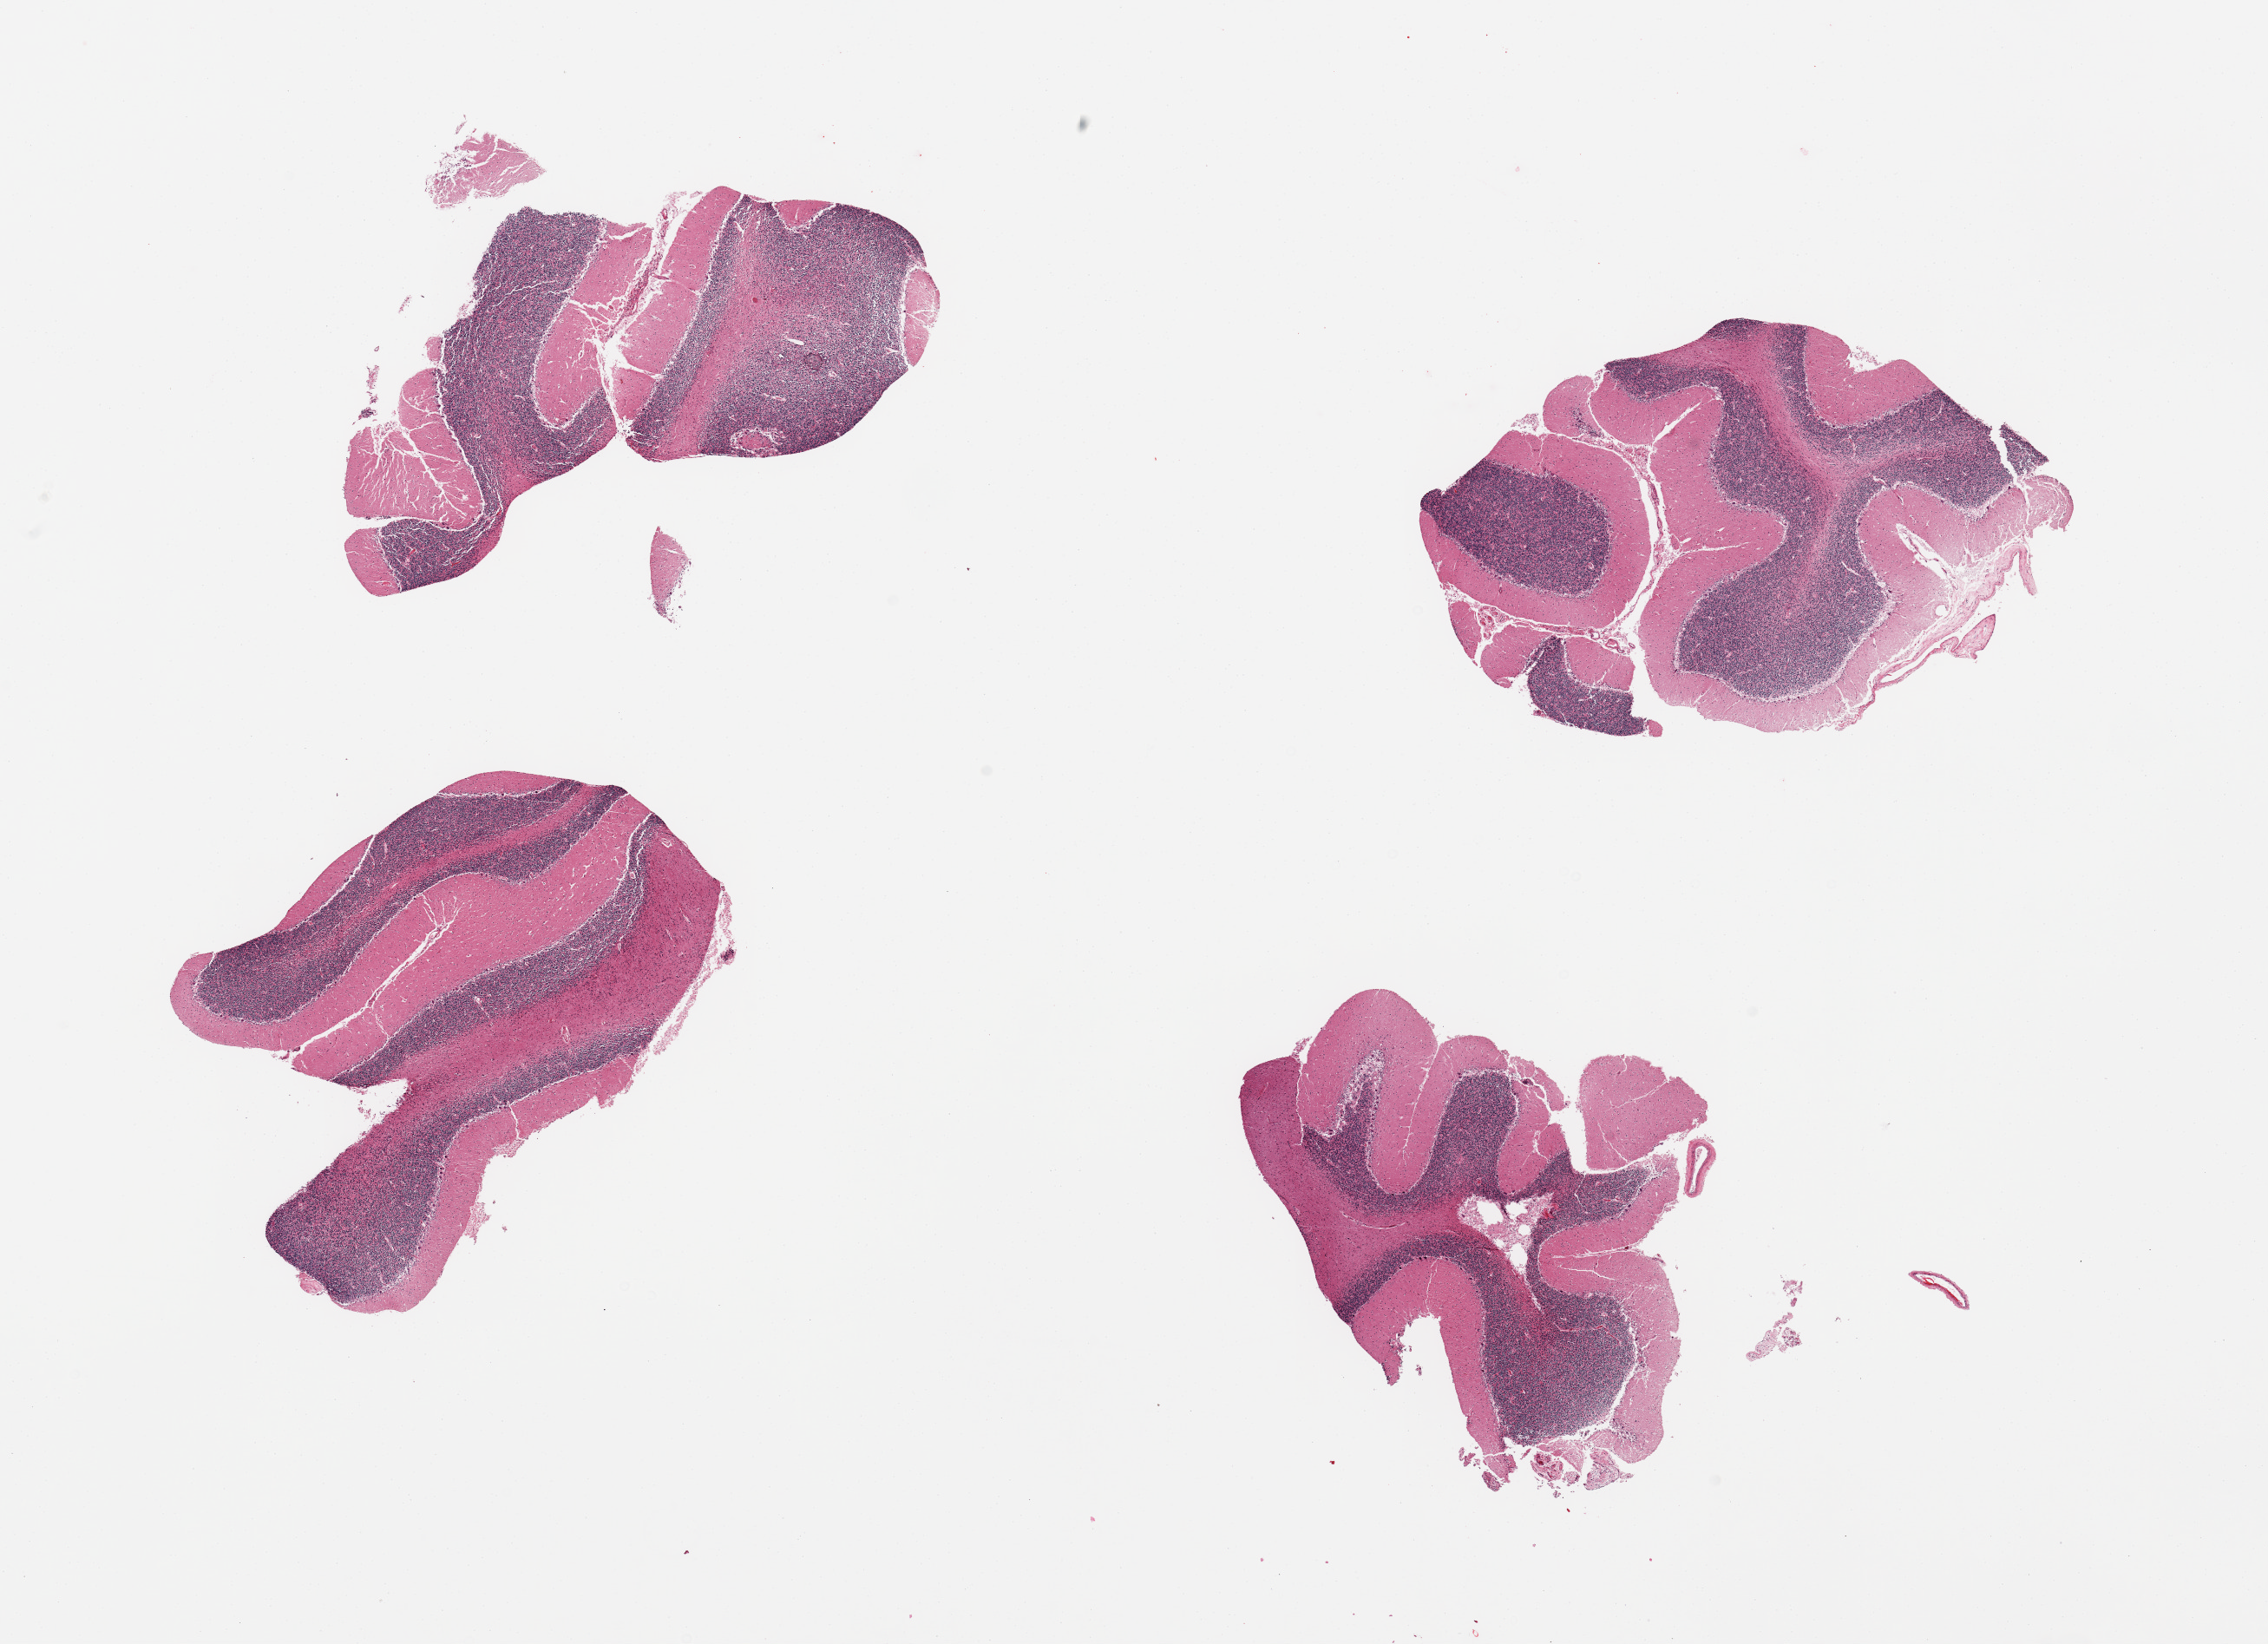
H&E whole-slide image, brightfield, low-resolution overview of the scanned area, about 20.7 x 15.0 mm (slide scanned at 20x); PAXgene-fixed, paraffin-embedded tissue; section of cerebellum (target tissue); donor tissue sample. Donor: male.
Pathologist's review note for this sample: 4 pieces.